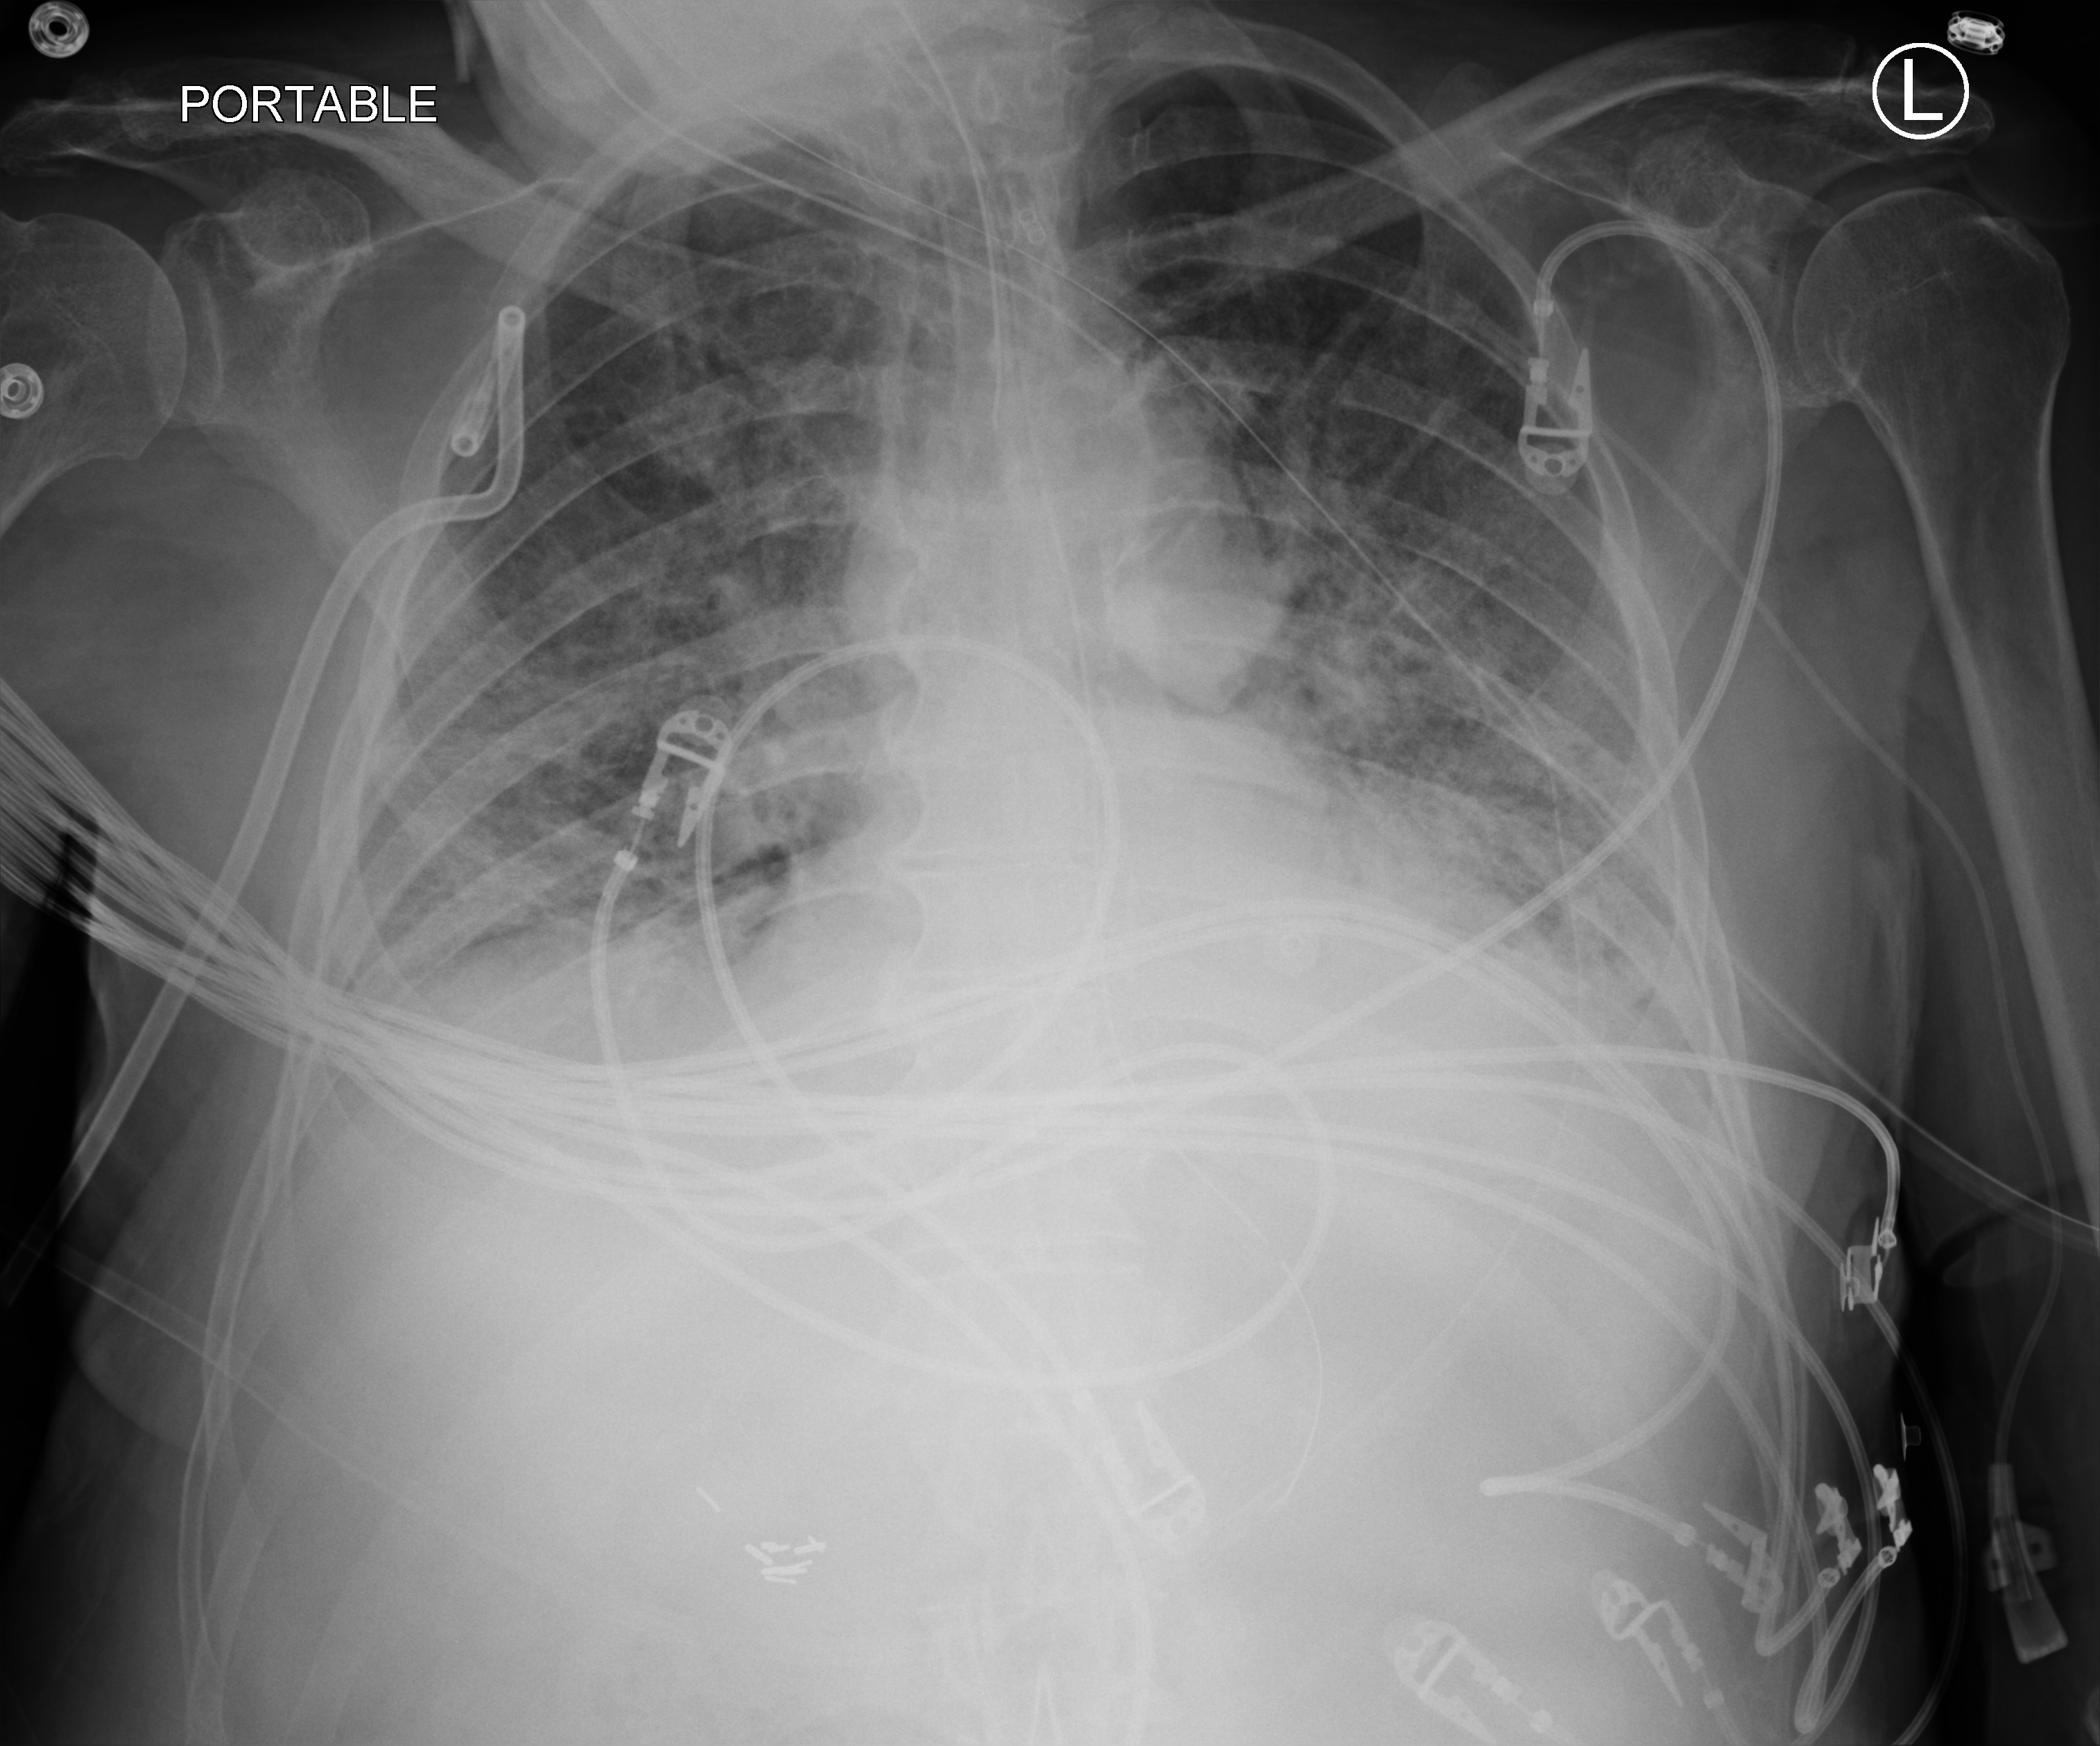
Portable chest radiograph; anteroposterior (AP) projection. Patient hospitalised with COVID-19; male, aged 75–90 years.
Hospital-stay facts (about this admission, not read from this image; timing relative to this image not recorded): mechanically ventilated during this hospital stay: yes.